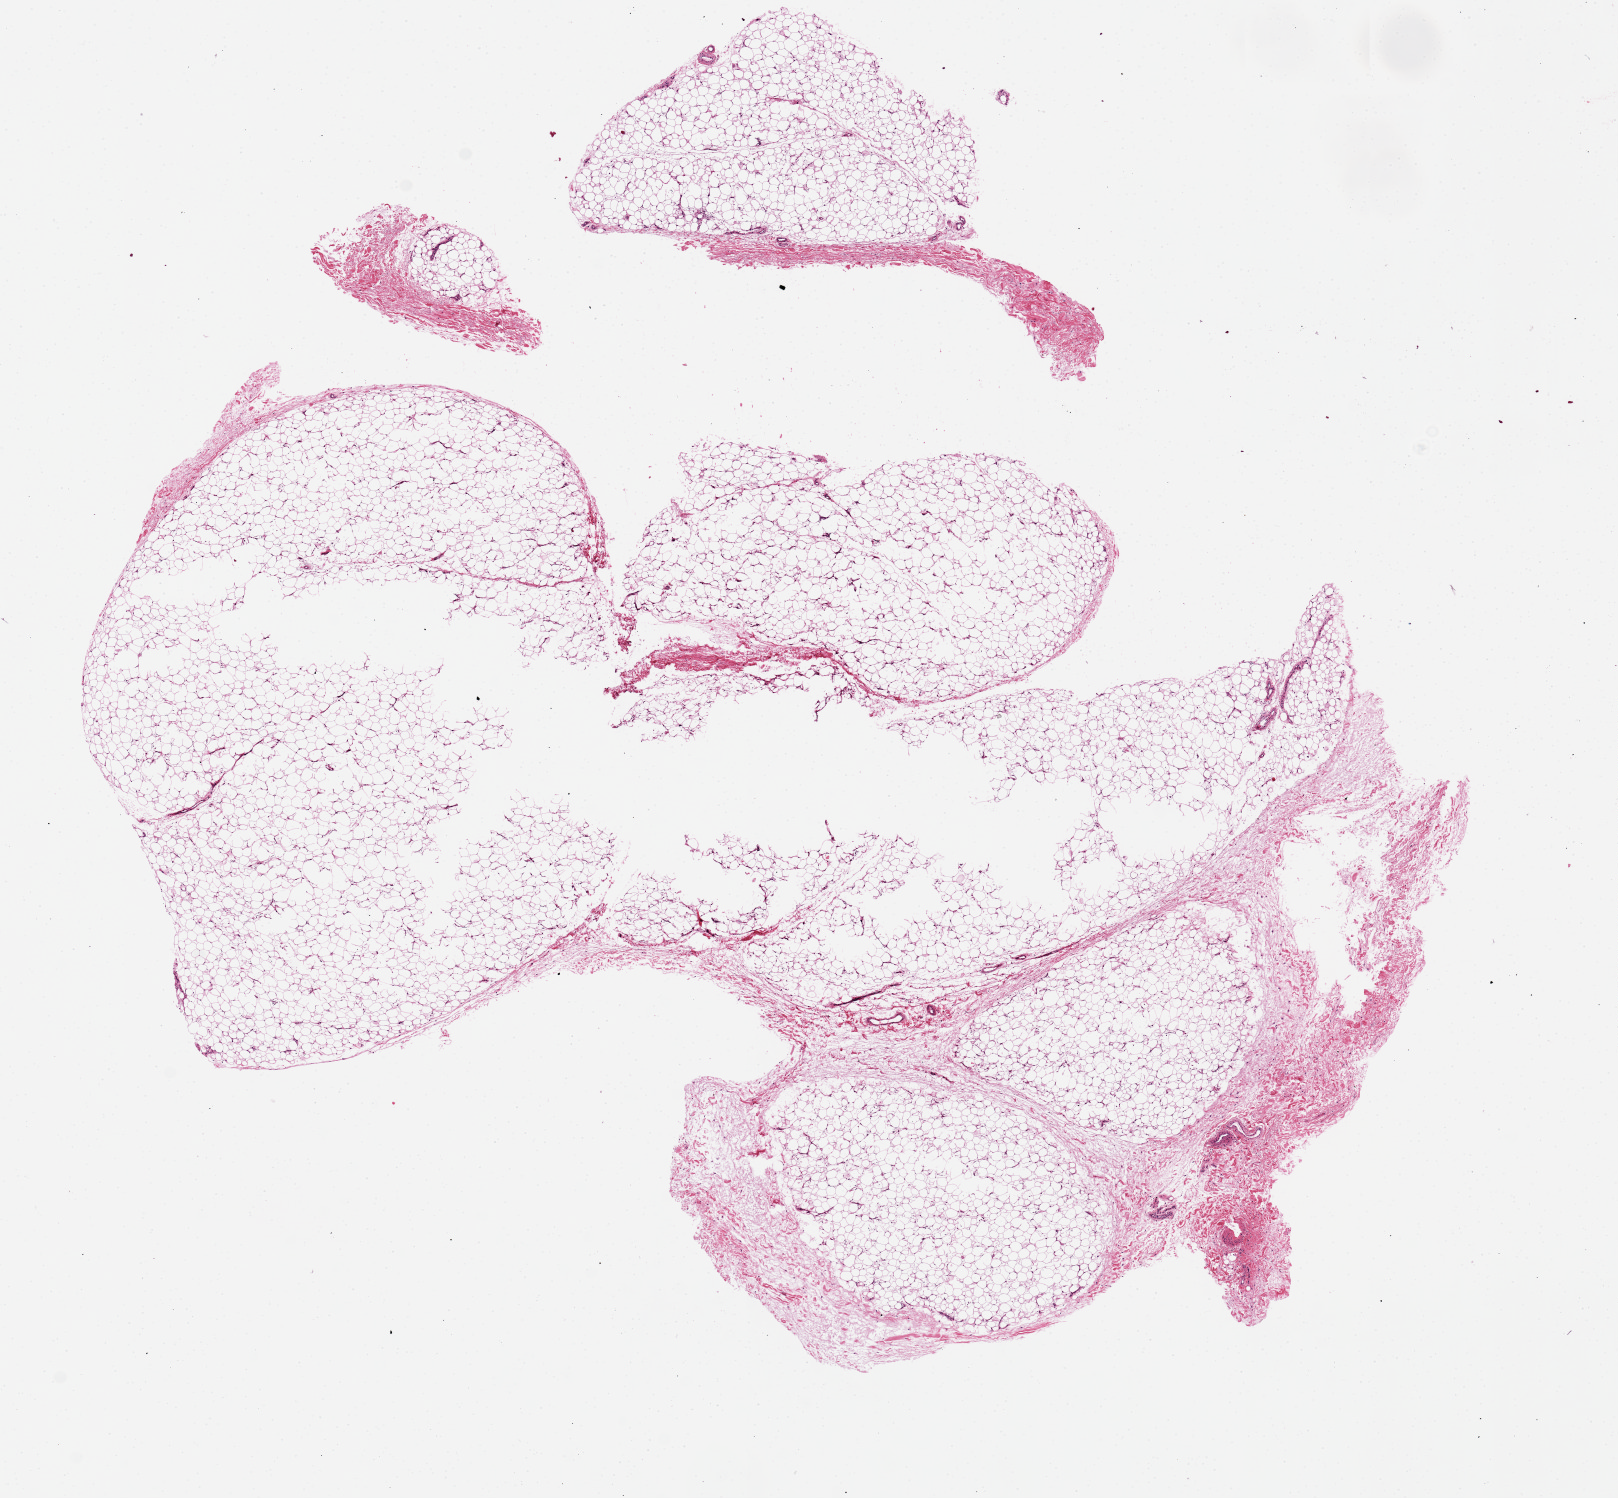
Digitized haematoxylin and eosin-stained section — shown as a low-resolution overview of the whole scanned area (about 12.8 x 11.8 mm, from a 20x scan); PAXgene-fixed paraffin-embedded (PFPE) section; section of adipose tissue (target tissue); donor tissue sample. Female donor.
Review note (as recorded): Poor fixation centrally. Specimen averages 10mm x 5-7mm.